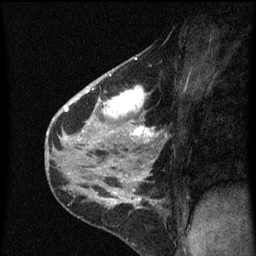
Breast MRI (dynamic contrast-enhanced), one sagittal slice. Slice 39 of 60 in the series (ordered by position). Dynamic contrast-enhanced series, image 2 of 3 at this slice position (ordered by acquisition). 1.5 T. TE 4.2 ms, TR 8 ms. 2 mm slice thickness. 256 × 256 image matrix, field of view 180 × 180 mm. Patient: female, 38 years.
Annotated regions visible in this slice (semi-automatic segmentation, software-assisted and operator-edited):
- analysis volume of interest (the breast-tissue region the enhancement analysis was run in; not a lesion): bounding box [x1, y1, x2, y2] px = [80, 54, 165, 151]
- tumour enhancement mask (voxels above the 70 % enhancement threshold inside the analysis volume of interest): [82, 58, 159, 143]